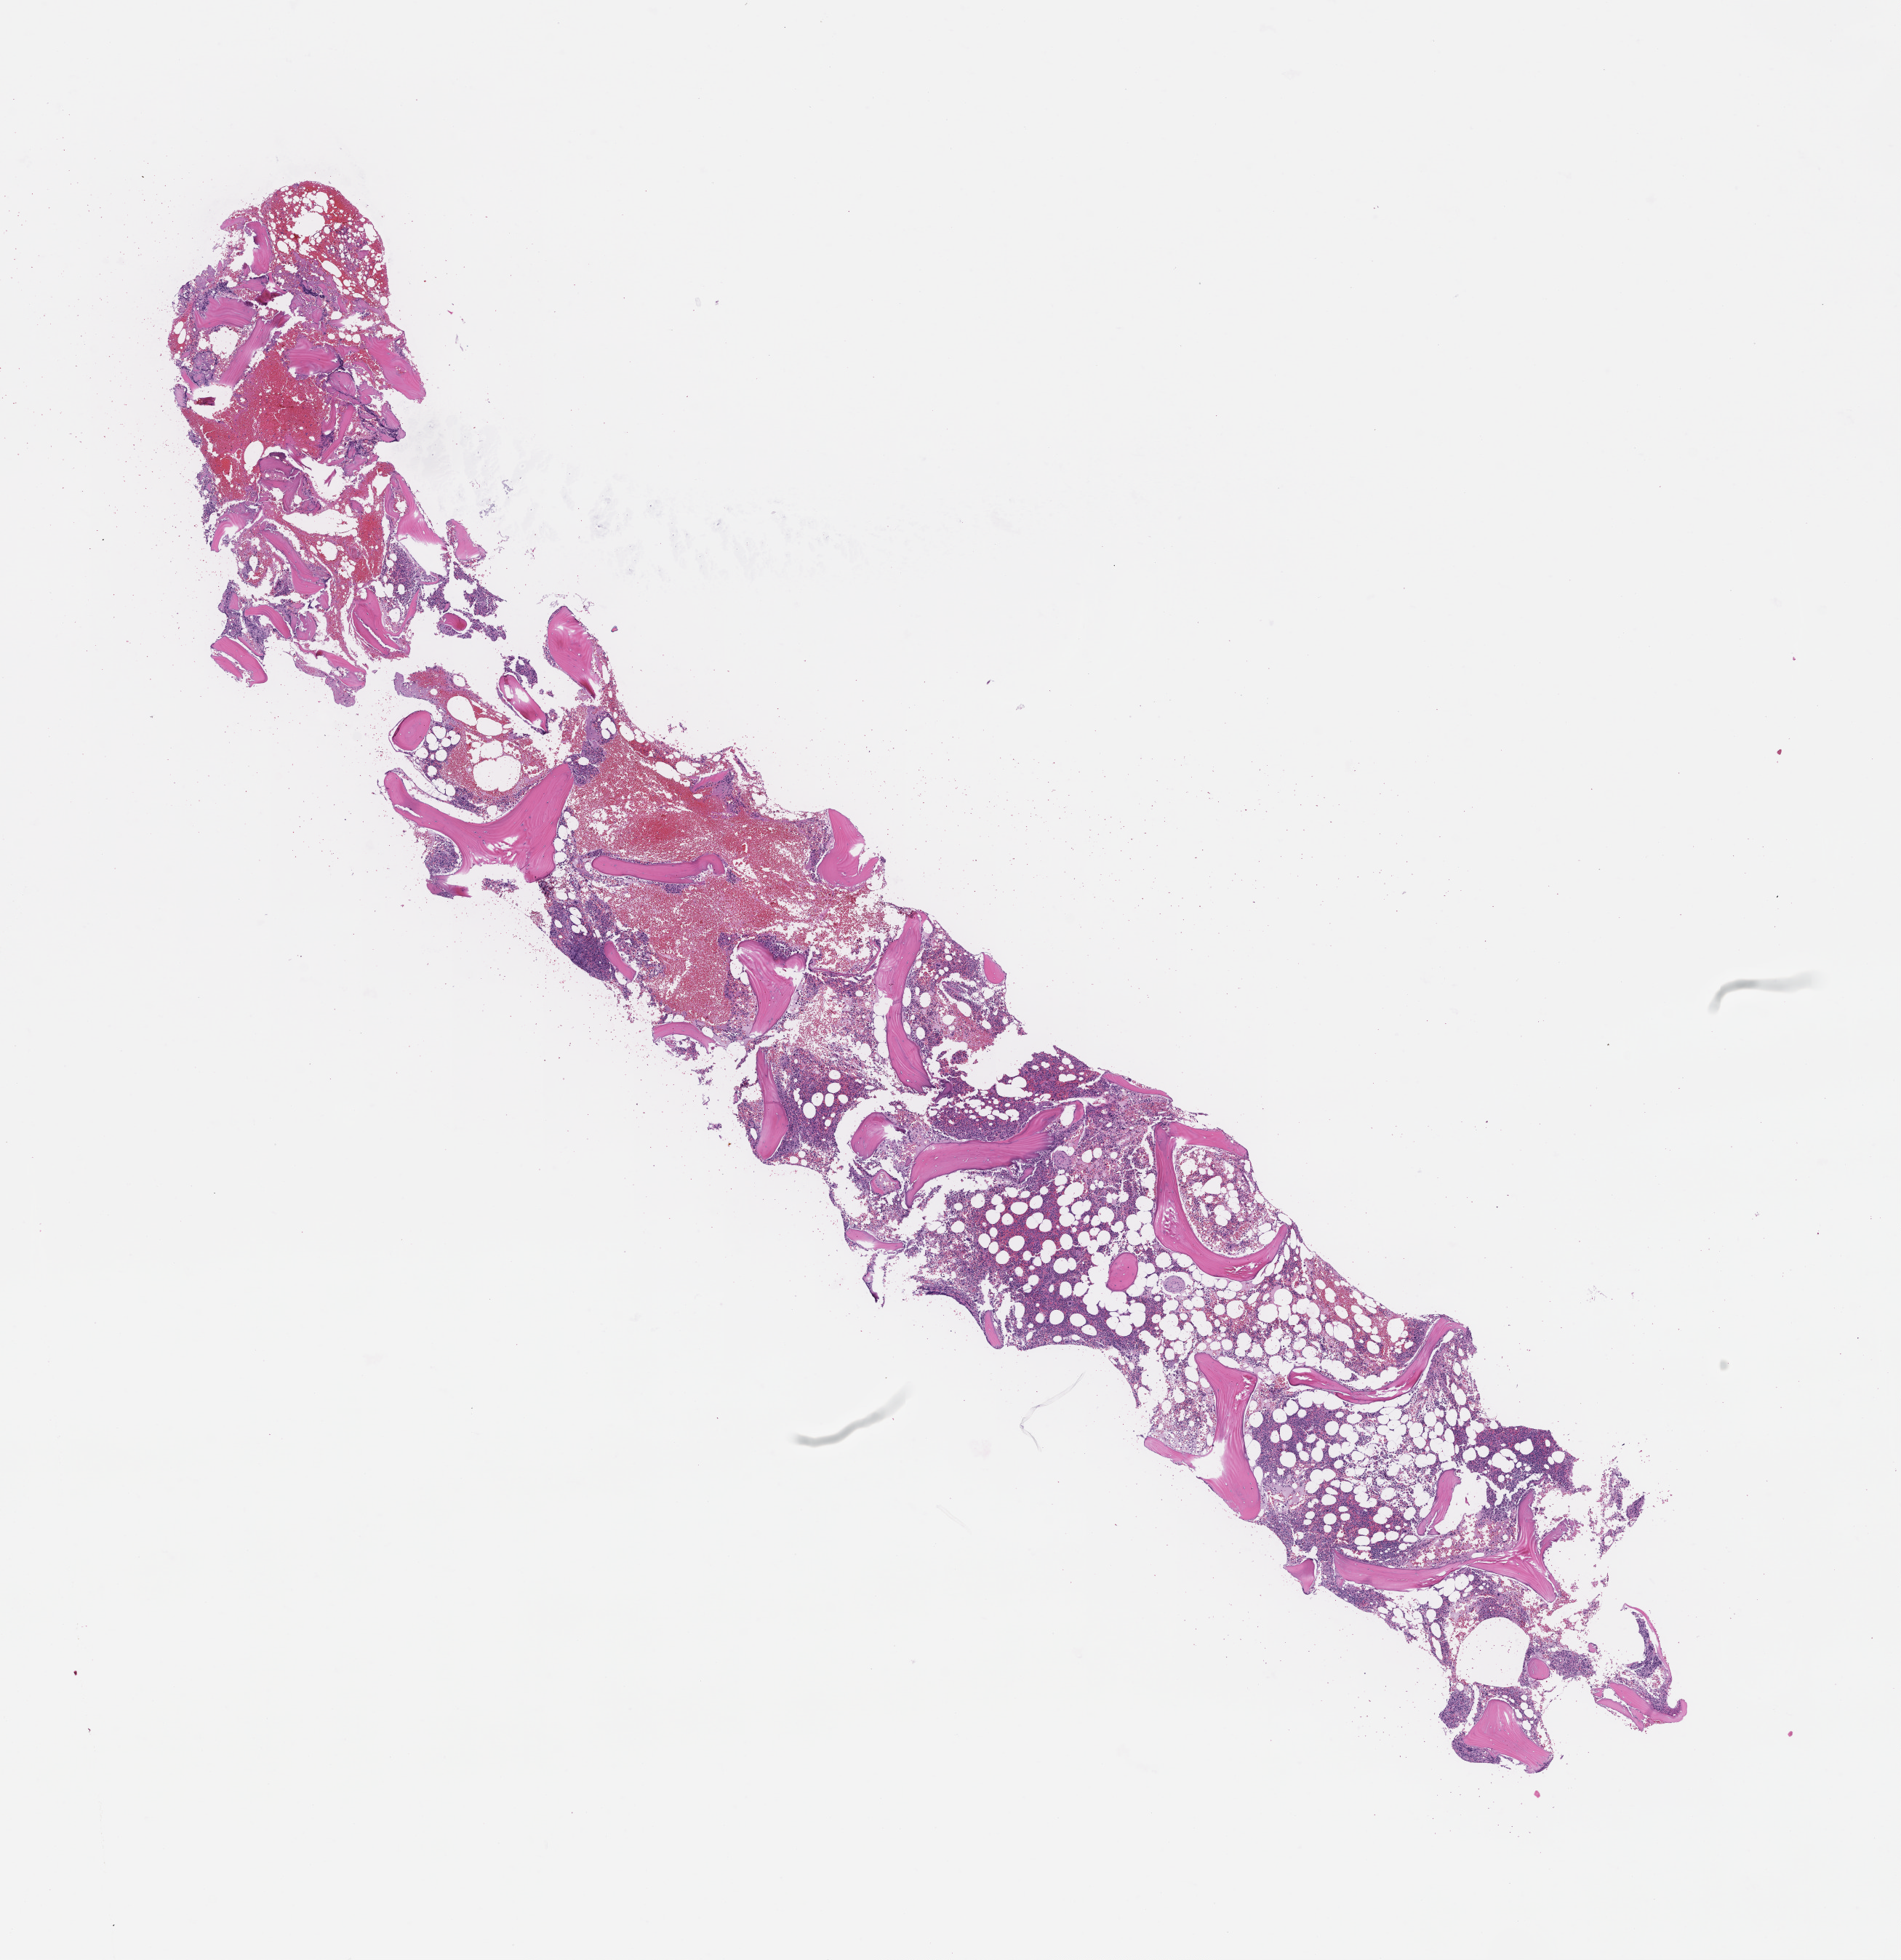
Digitized hematoxylin and eosin (H&E)-stained section, low-resolution overview of the scanned area, about 10.6 x 10.9 mm; formalin-fixed, paraffin-embedded (FFPE) tissue; site: bone marrow; specimen time point: archival tissue. Patient: male.
This section: primary tumour tissue. Diagnosis: Plasma Cell Myeloma.